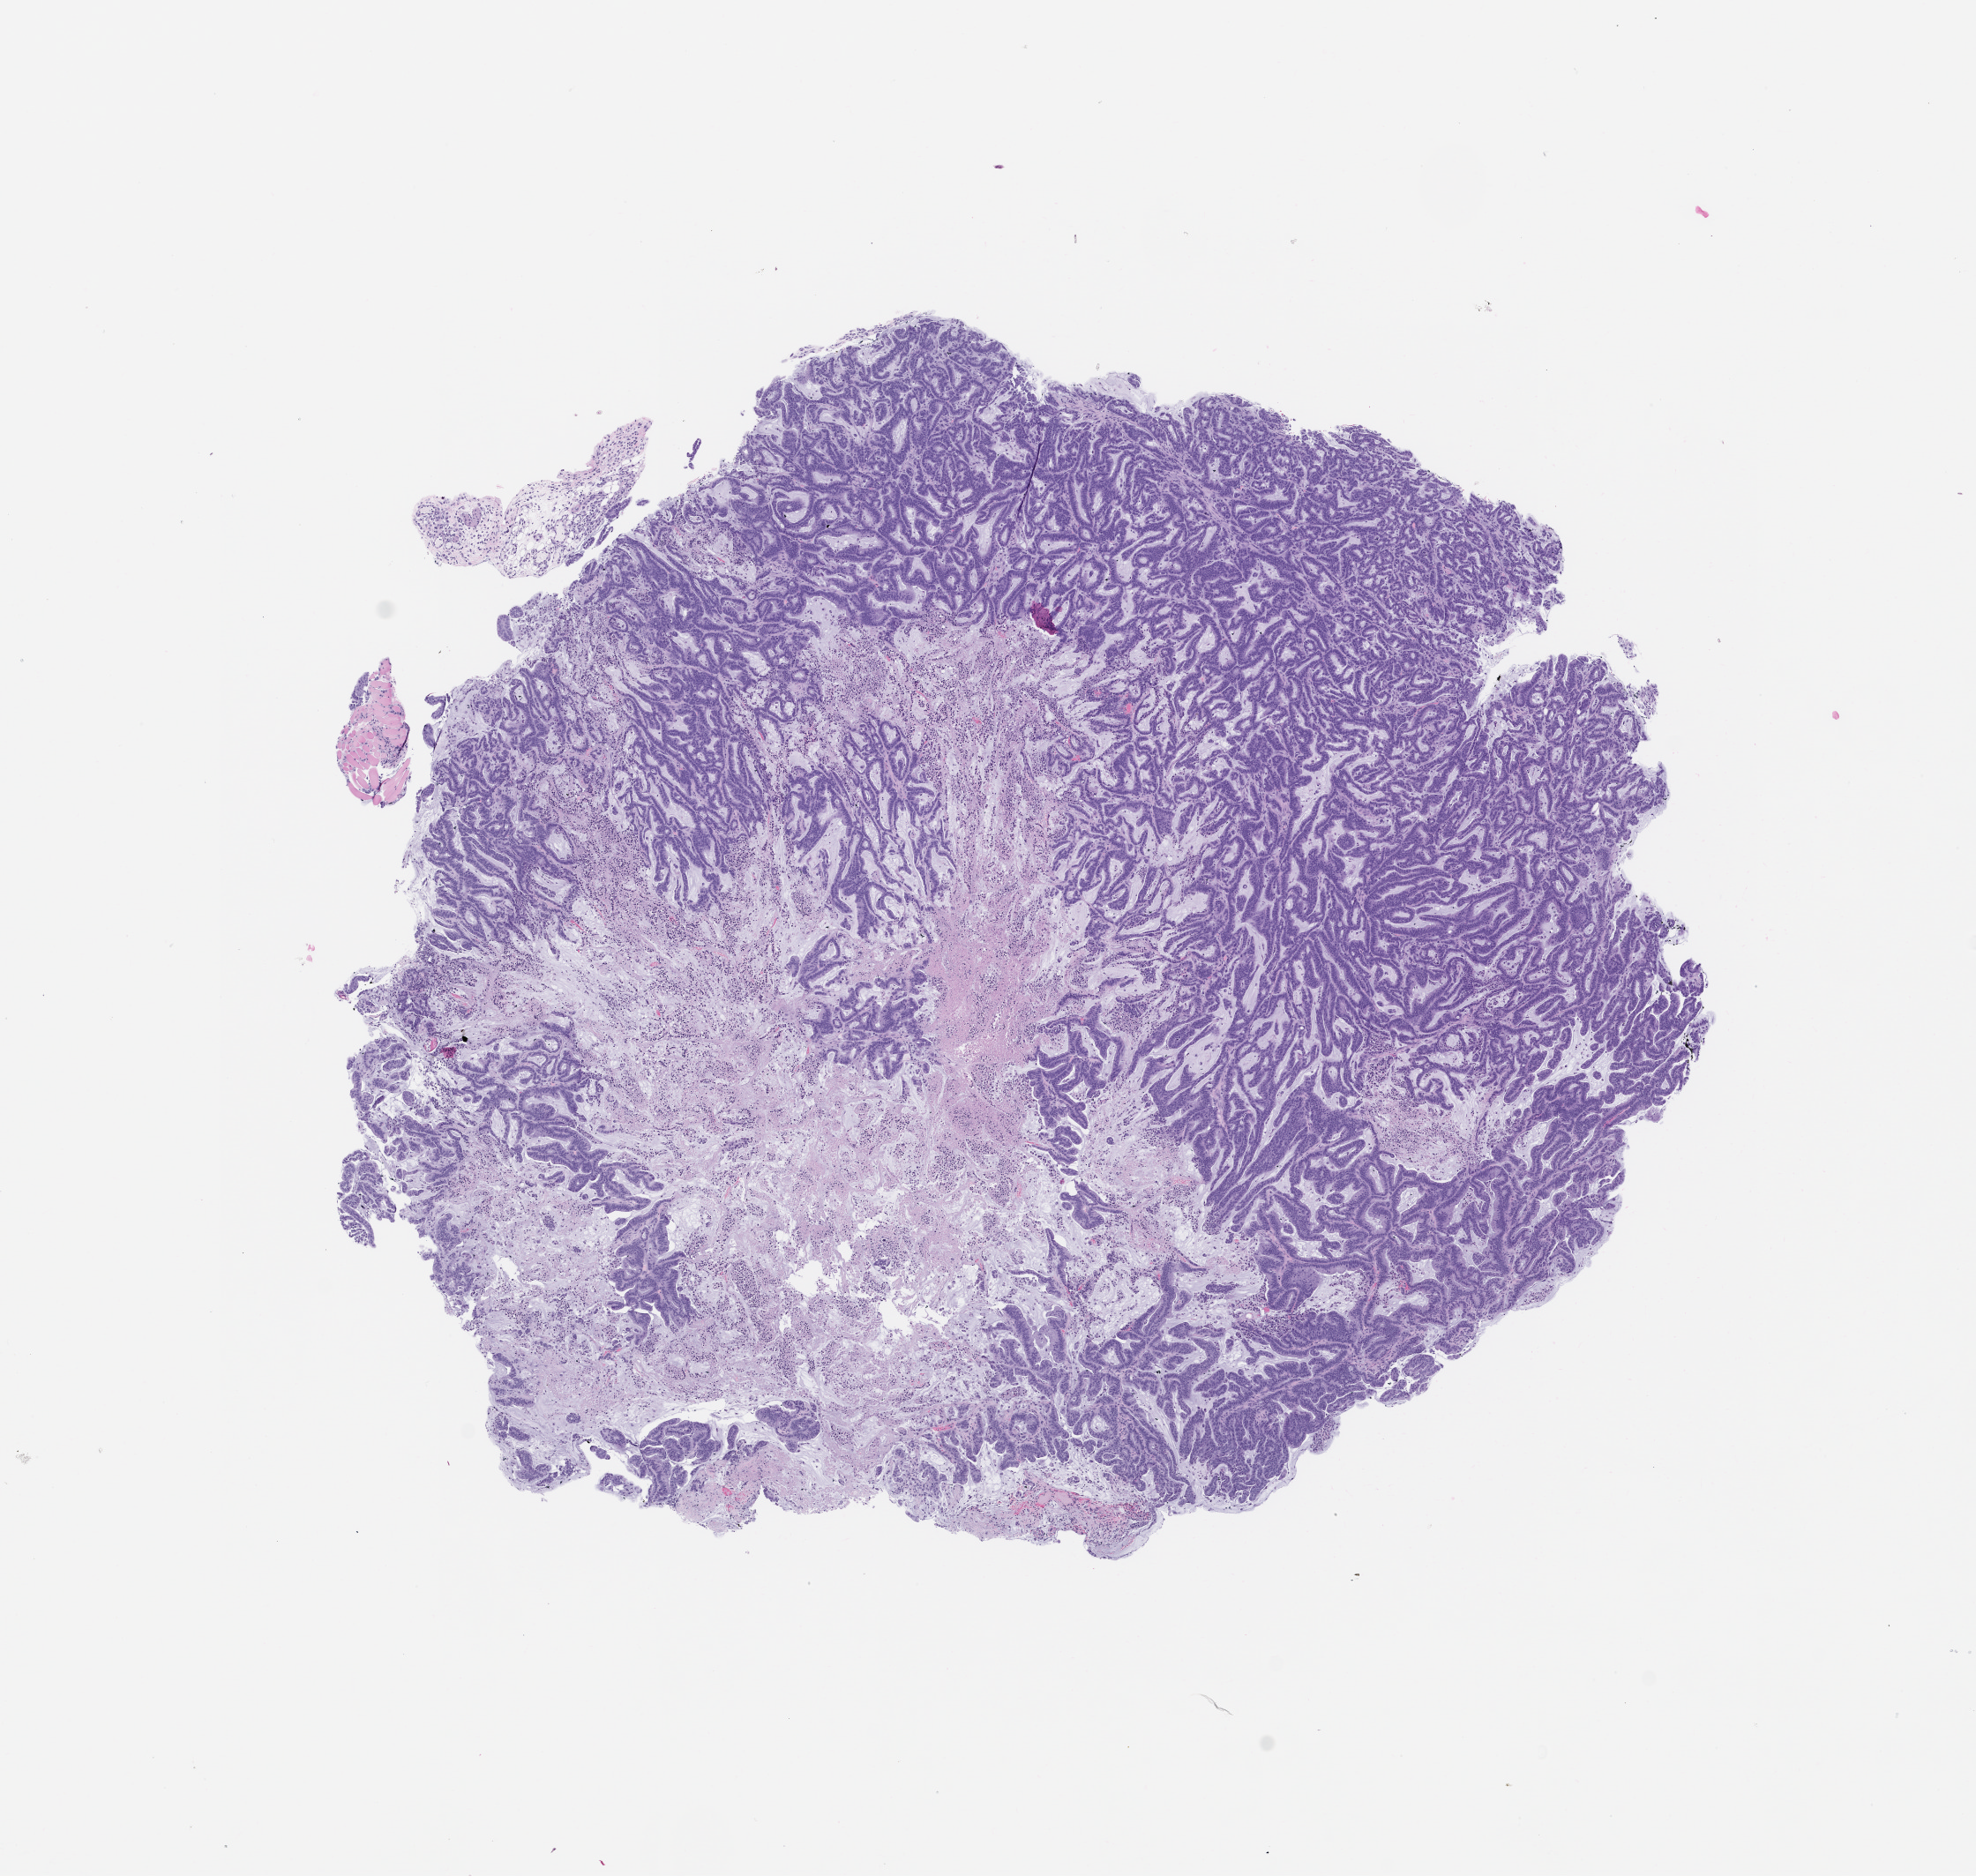
Haematoxylin and eosin whole-slide image of a patient-derived xenograft (PDX) tumor grown in a mouse, passage 1, shown as a low-resolution overview of the whole scanned area (about 9.0 x 8.5 mm). FFPE section. Originating tumor site category: colon.
Originating patient diagnosis: Colon Adenocarcinoma.